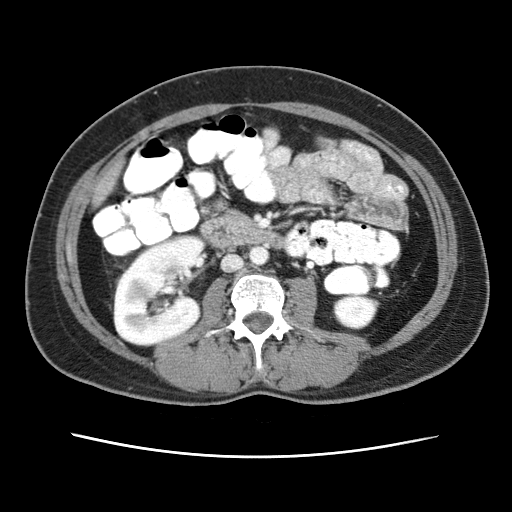
Contrast-enhanced abdominal CT (liver protocol), one axial slice; slice 3 of 79 in the series (ordered by position); 120 kVp; soft-tissue window (W 400 / L 40 HU); 2.5 mm slice thickness; 512 × 512 image matrix, field of view 340 × 340 mm. Case-level facts recorded for this patient, not image findings: diagnosis: hepatocellular carcinoma (patient treated with transarterial chemoembolisation; whether this scan precedes or follows treatment is not stated here); TNM stage (as recorded): Stage-I; Child-Pugh class: A; tumour differentiation: moderately differentiated.
Structures marked on this image (semi-automatic segmentation, software-assisted and operator-edited):
- abdominal aorta: bounding box [x1, y1, x2, y2] px = [249, 247, 268, 266]
- liver parenchyma outside the tumour (the mass and vessels are separate outlines, so this box may not span the whole liver): [95, 160, 122, 200]